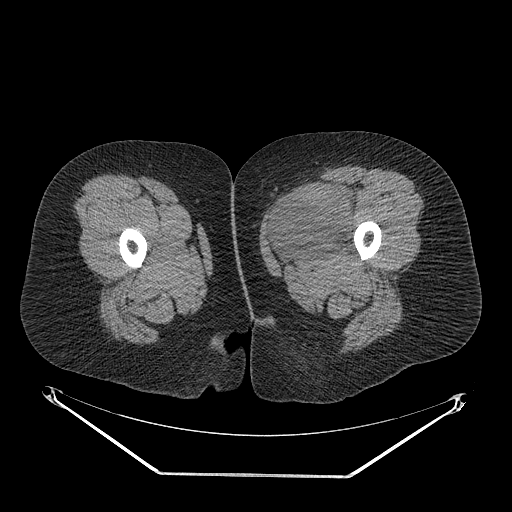
CT of an extremity soft-tissue mass (from a PET/CT study), one axial slice; slice 24 of 267 in the series (ordered by position); reconstruction kernel STANDARD; soft-tissue window (W 400 / L 40 HU); 3.75 mm slice thickness; 512 × 512 image matrix, field of view 500 × 500 mm. Female patient. From the clinical record (not read from this slice): histological type: myxofibrosarcoma; grade: intermediate; site of the primary tumour: left thigh.
Annotated regions visible in this slice (expert contour drawn on MRI and transferred to this co-registered scan by the dataset authors):
- gross tumour volume including surrounding oedema: bounding box (x1, y1, x2, y2) in pixels: (267, 183, 355, 259)
- gross tumour volume (mass): (269, 189, 353, 254)